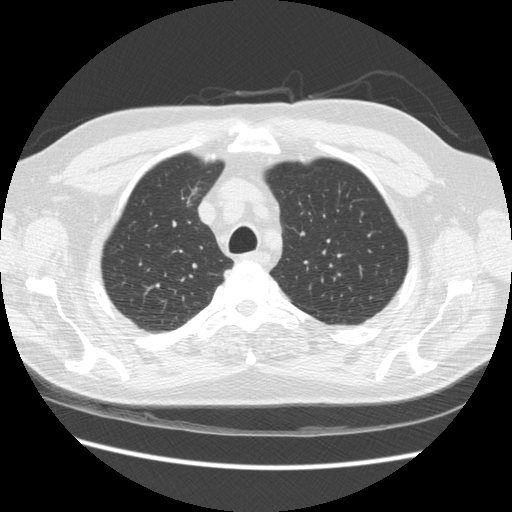
Axial slice from a low-dose chest CT screening exam; third annual screen; lung window (W 1500 / L -600 HU); 2.5 mm slice thickness; standard (soft-tissue) reconstruction kernel (STANDARD); 512 × 512 image matrix, field of view 360 × 360 mm. Male participant, aged 66 years at enrolment. Former smoker at enrolment.
- Lesion marked by an expert reader, box from (x=164, y=173) to (x=215, y=219) px.
- Screening reader's record for this exam: no non-calcified nodule ≥4 mm recorded.
- Official screen result: positive, other.
- Participant outcome: lung cancer diagnosed 229 days after this screen — bronchiolo-alveolar adenocarcinoma, NOS, right upper lobe, moderately differentiated (G2), stage IA (AJCC 6th edition), 12 mm at pathology.